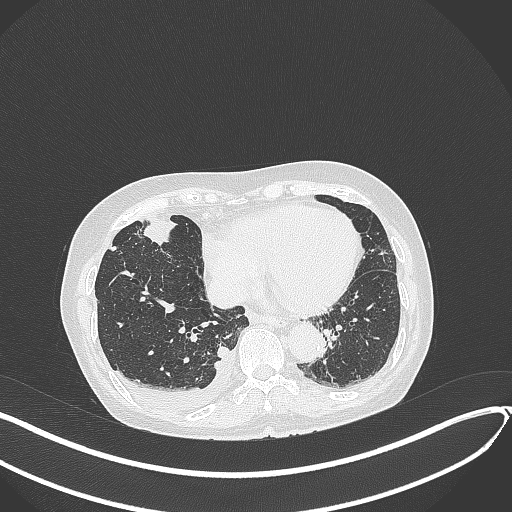
Chest CT, one axial slice; position 120 of 418 along the scan axis; 120 kVp; lung window (W 1500 / L -600 HU); 512 × 512 image matrix. Patient: female, 75 years. Case-level facts recorded for this patient, not image findings: clinical TNM (as recorded): T2a N3 M0.
Outlined on this slice (bounding box drawn by a radiologist):
- lung tumour (recorded histology: adenocarcinoma): bounding box <134,209,182,250> (left, top, right, bottom; pixels)